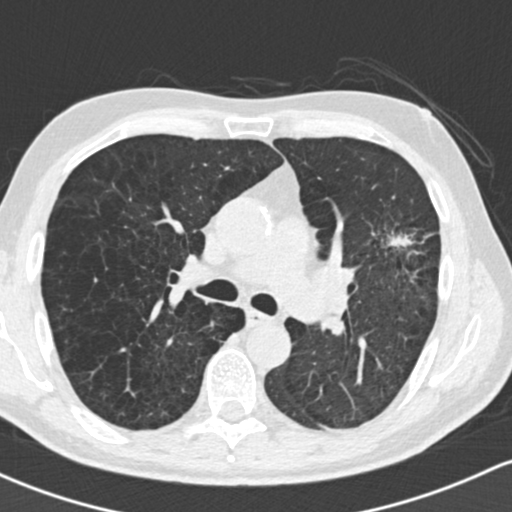
Low-dose screening chest CT, one axial slice; slice 94 of 162 in the series (ordered by position); lung window (W 1500 / L -600 HU); 2 mm slice thickness; 512 × 512 image matrix, field of view 318 × 318 mm.
Outlined on this slice (expert manual segmentation):
- lesion 1 (tumor, upper lobe of left lung): bounding box <387,234,413,248> (left, top, right, bottom; pixels)